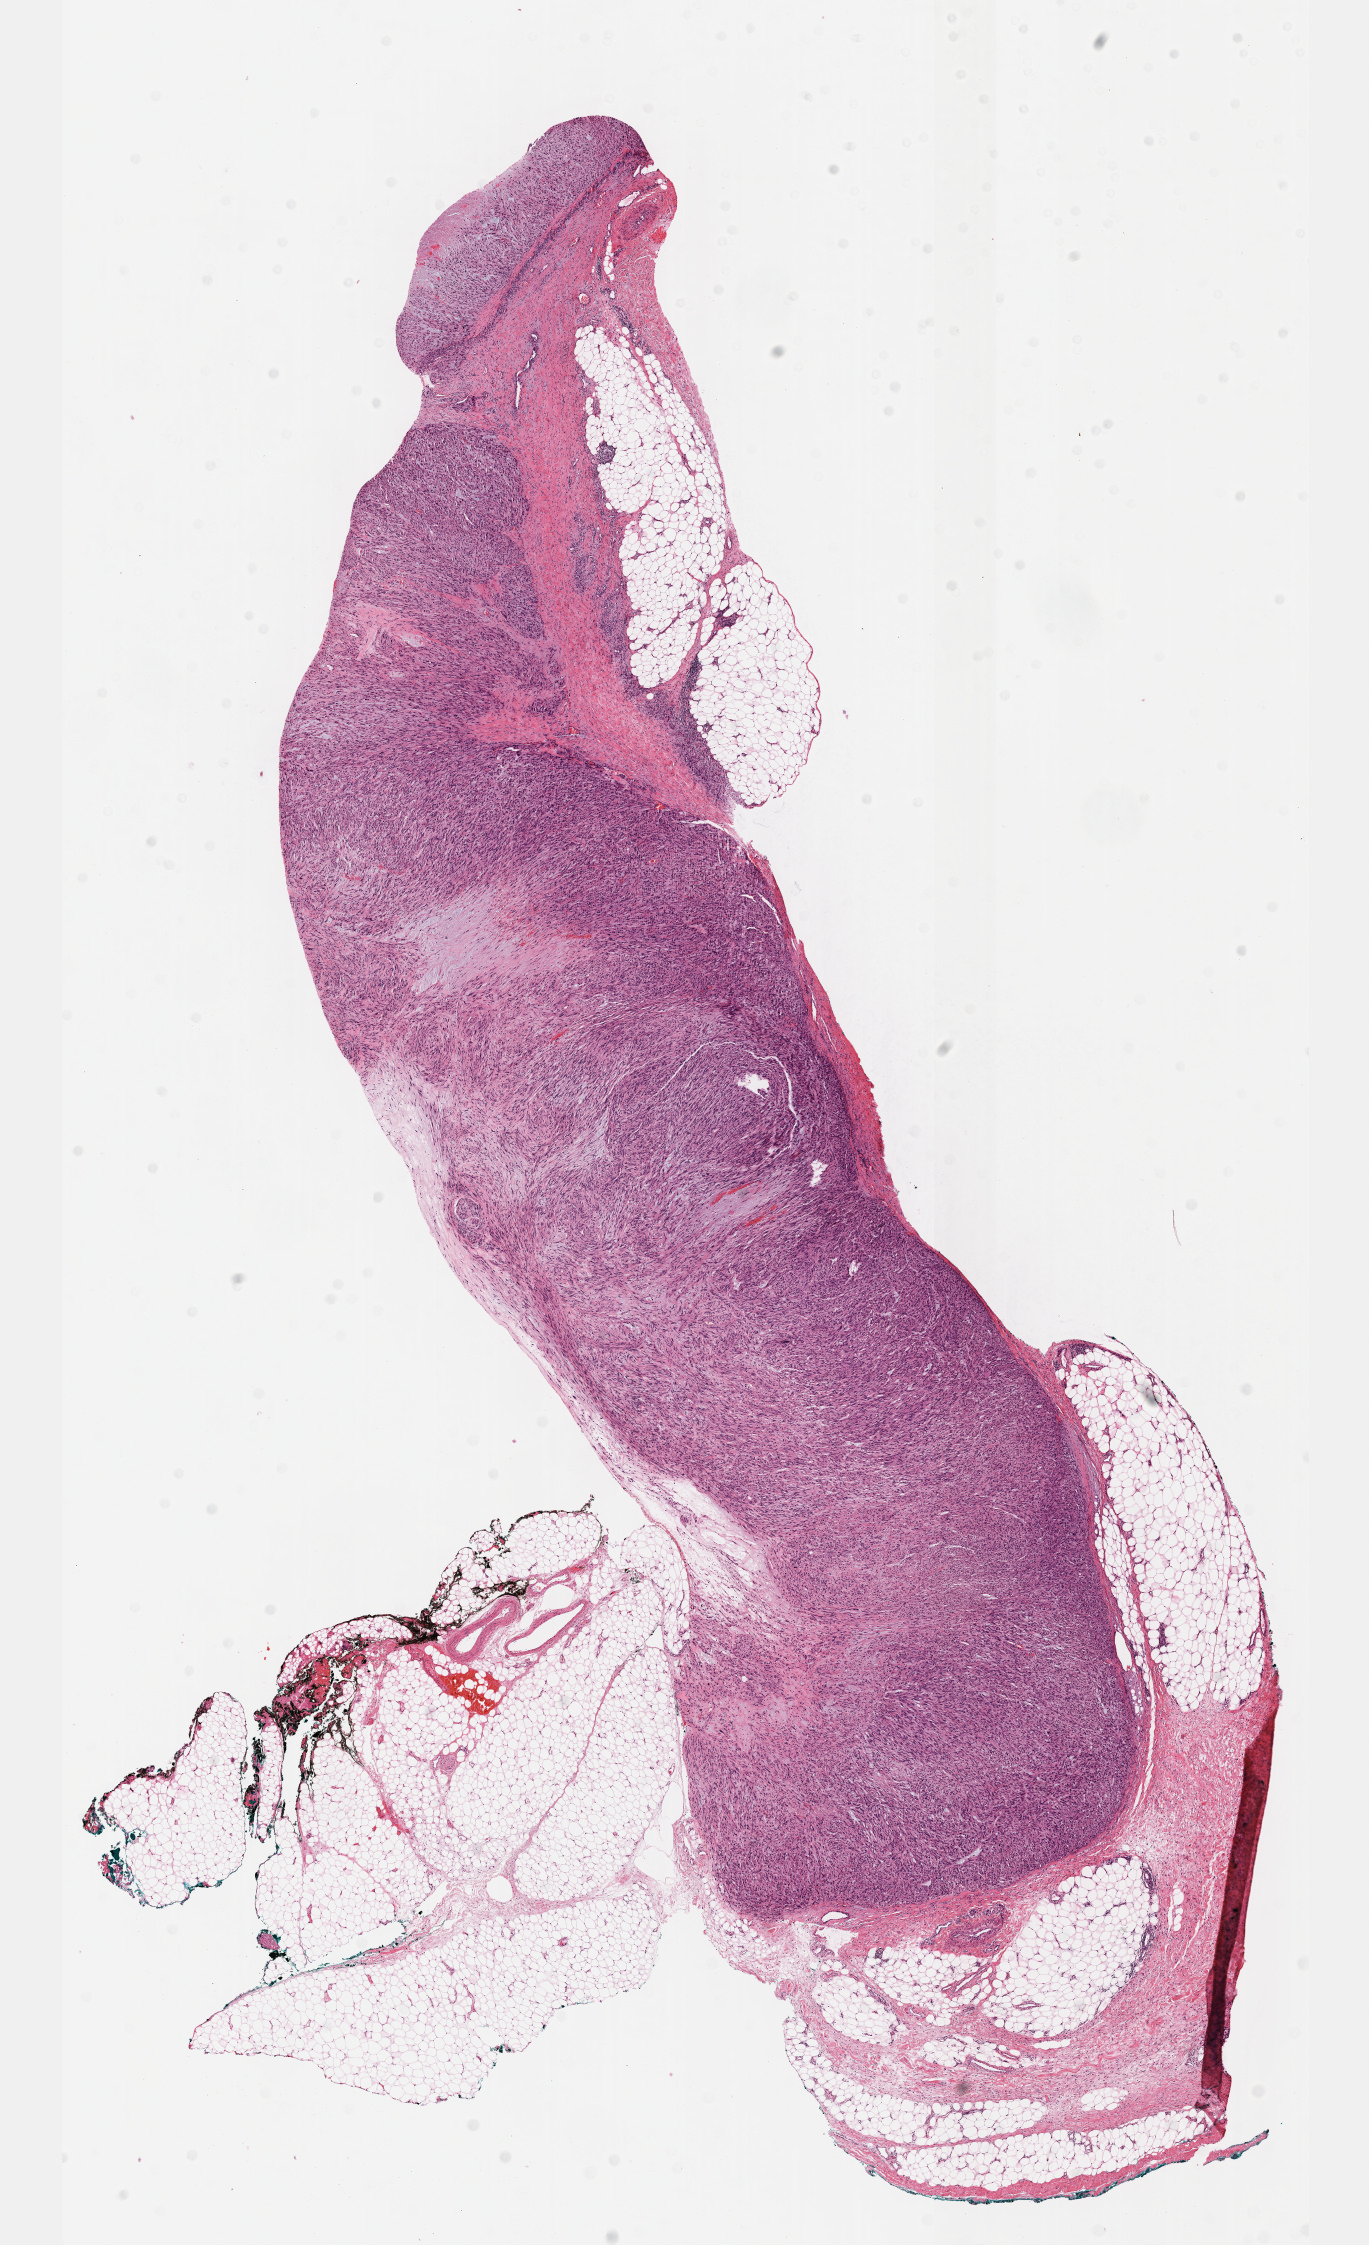
Whole-slide histology image, H&E, shown as a low-resolution overview of the whole scanned area (about 11.1 x 18.1 mm, from a 40x scan). Formalin-fixed paraffin-embedded (FFPE) diagnostic section. Sample: primary tumour, connective, subcutaneous and other soft tissues. Patient: female, age at initial diagnosis 63 years.
• diagnosis: Leiomyosarcoma, NOS (connective, subcutaneous and other soft tissues of lower limb and hip)